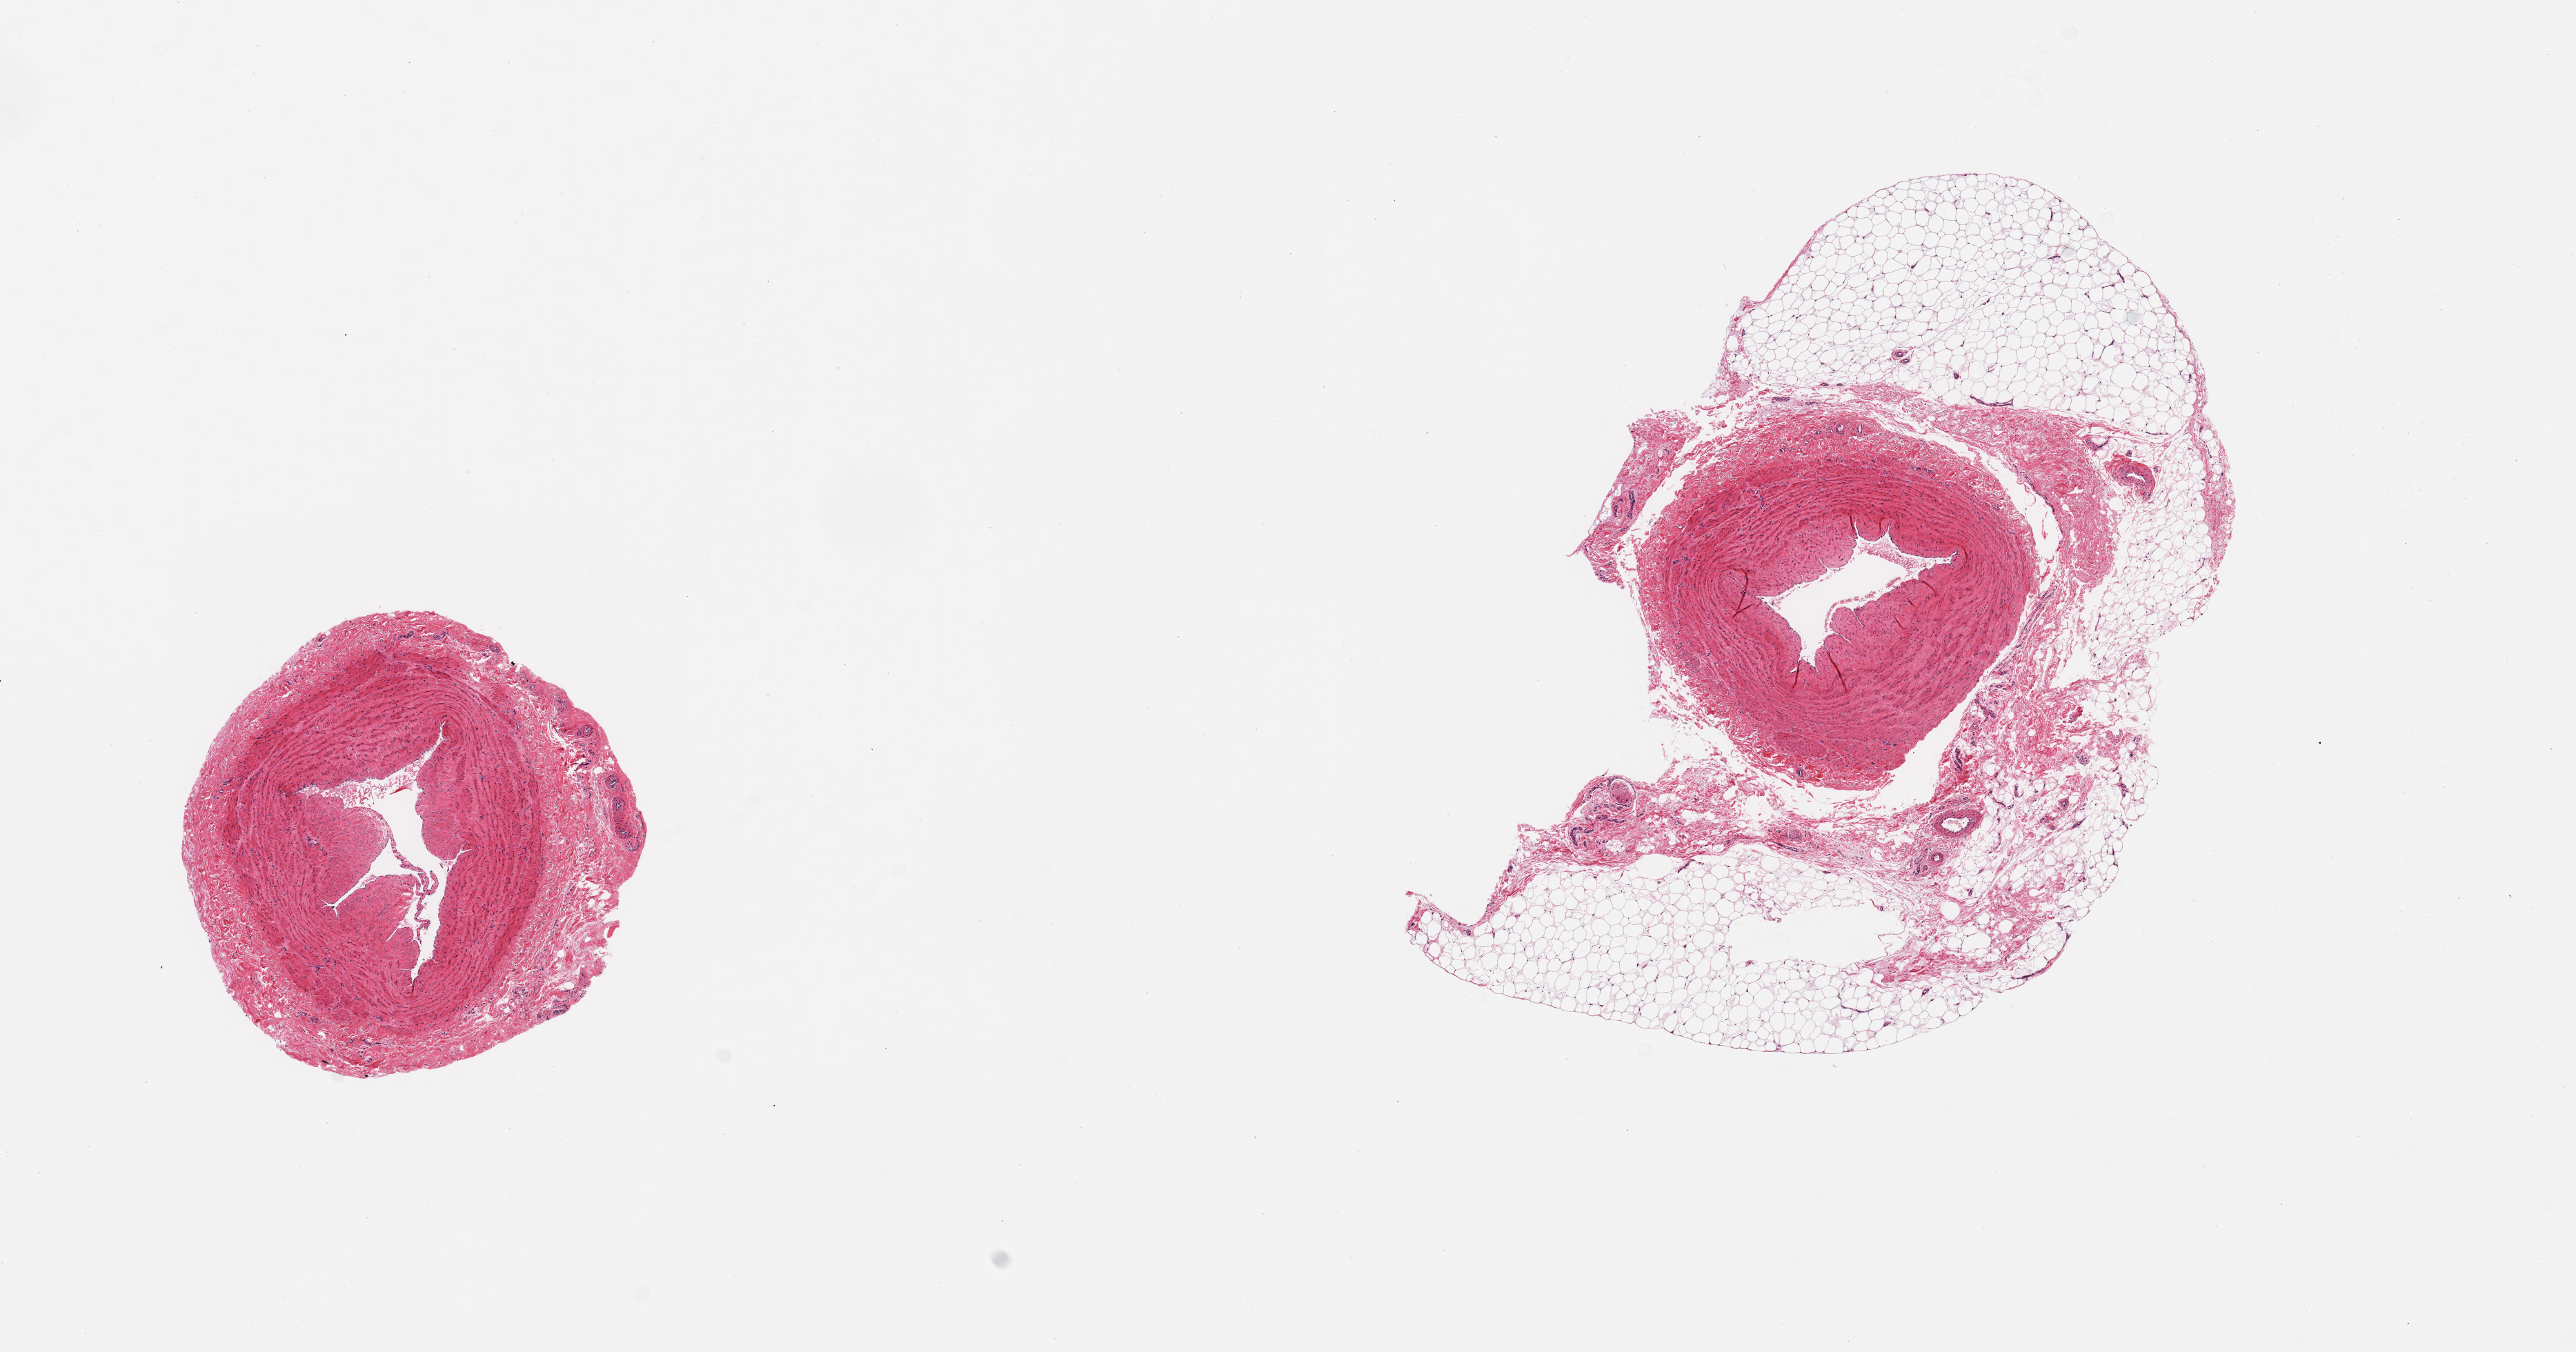
Digitized H&E-stained section, brightfield, whole scanned area (about 14.8 x 7.8 mm, acquisition: 20x scan) shown as a low-resolution overview, PAXgene-fixed, paraffin-embedded tissue, sampled site (target tissue): tibial artery, tissue donor sample. Male donor.
- review note (as recorded): 2 pieces; 1 piece includes ~70% attached fat